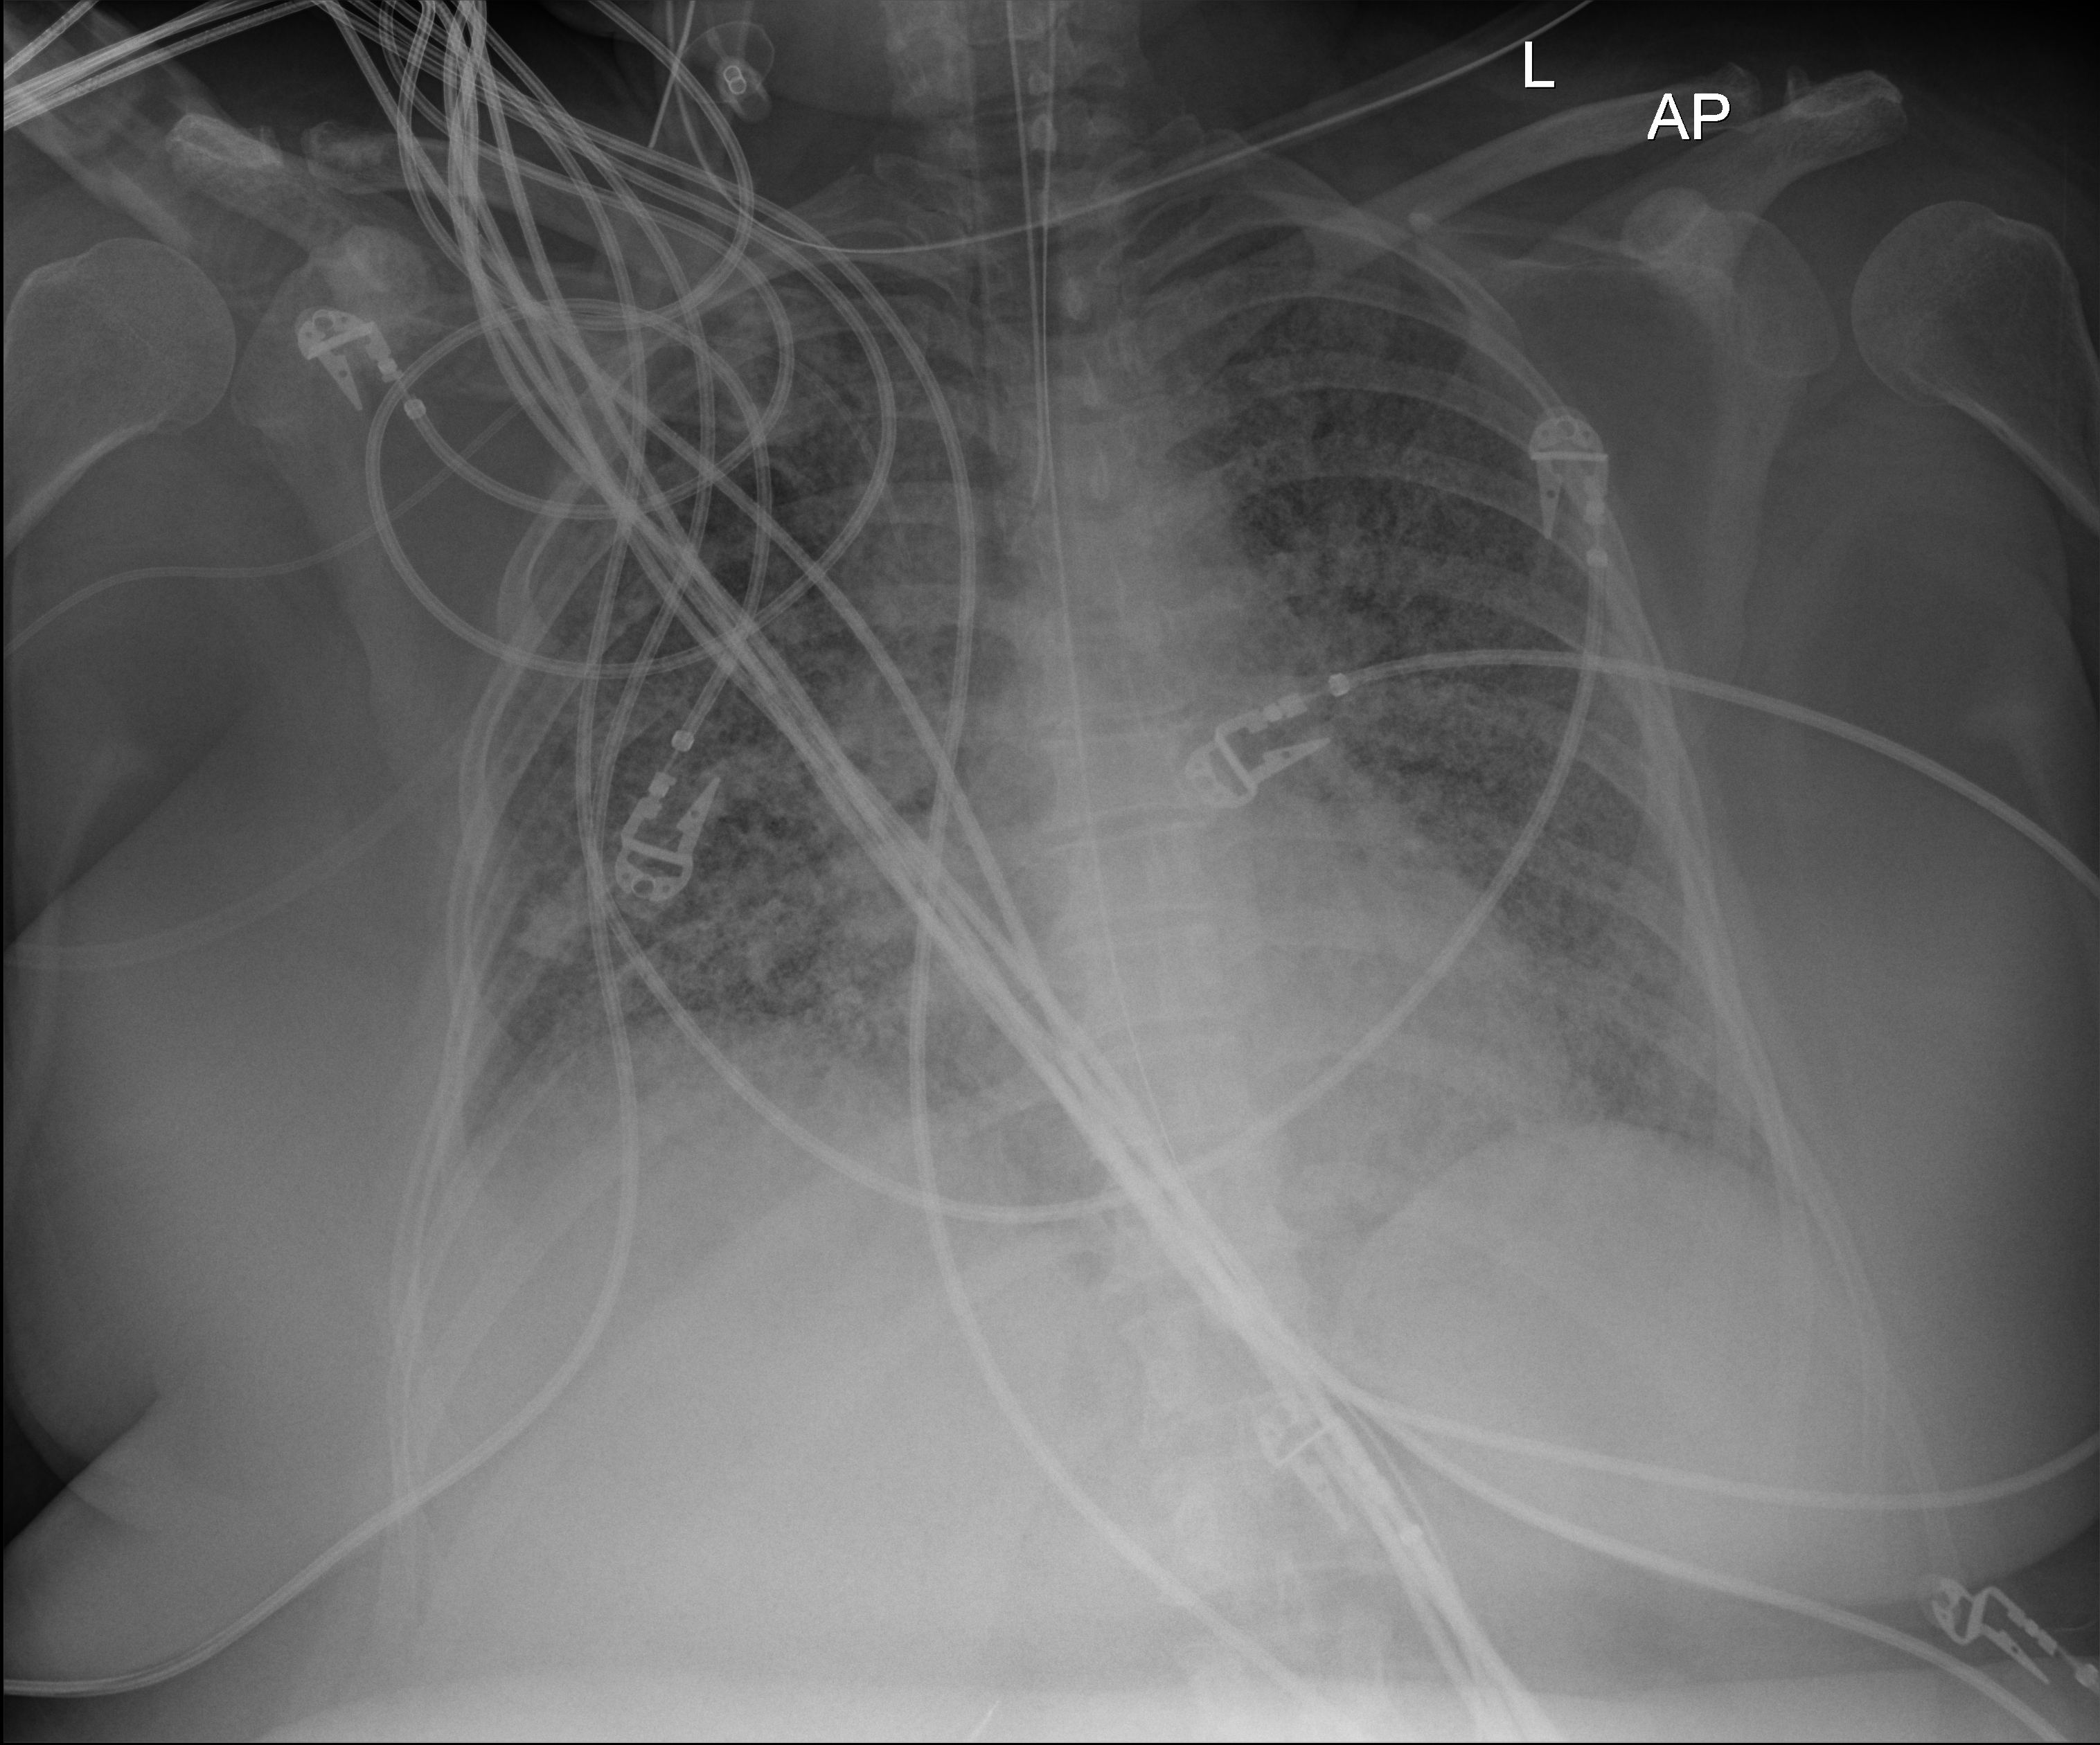
Portable chest radiograph; anteroposterior (AP) projection. Female patient hospitalised with COVID-19, age 18–59 years.
Admission-level facts for this patient (not findings on this image; timing relative to this image not recorded):
- COPD (admission record): no
- chronic kidney disease (admission record): no
- admitted to intensive care during this hospital stay: yes